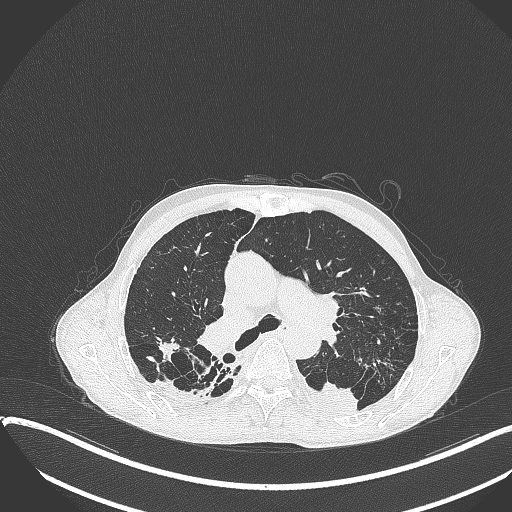
Chest CT, one axial slice; slice 253 of 401 in the series (ordered by position); reconstruction kernel B70f; lung window (W 1500 / L -600 HU); 512 × 512 image matrix, field of view 400 × 400 mm. Male patient, age 57 years. From the clinical record (not read from this slice): clinical TNM (as recorded): T4 N0 M0.
Structures marked on this image (bounding box drawn by a radiologist):
- lung tumour (recorded histology: squamous cell carcinoma): box from (x=305, y=376) to (x=362, y=419) px